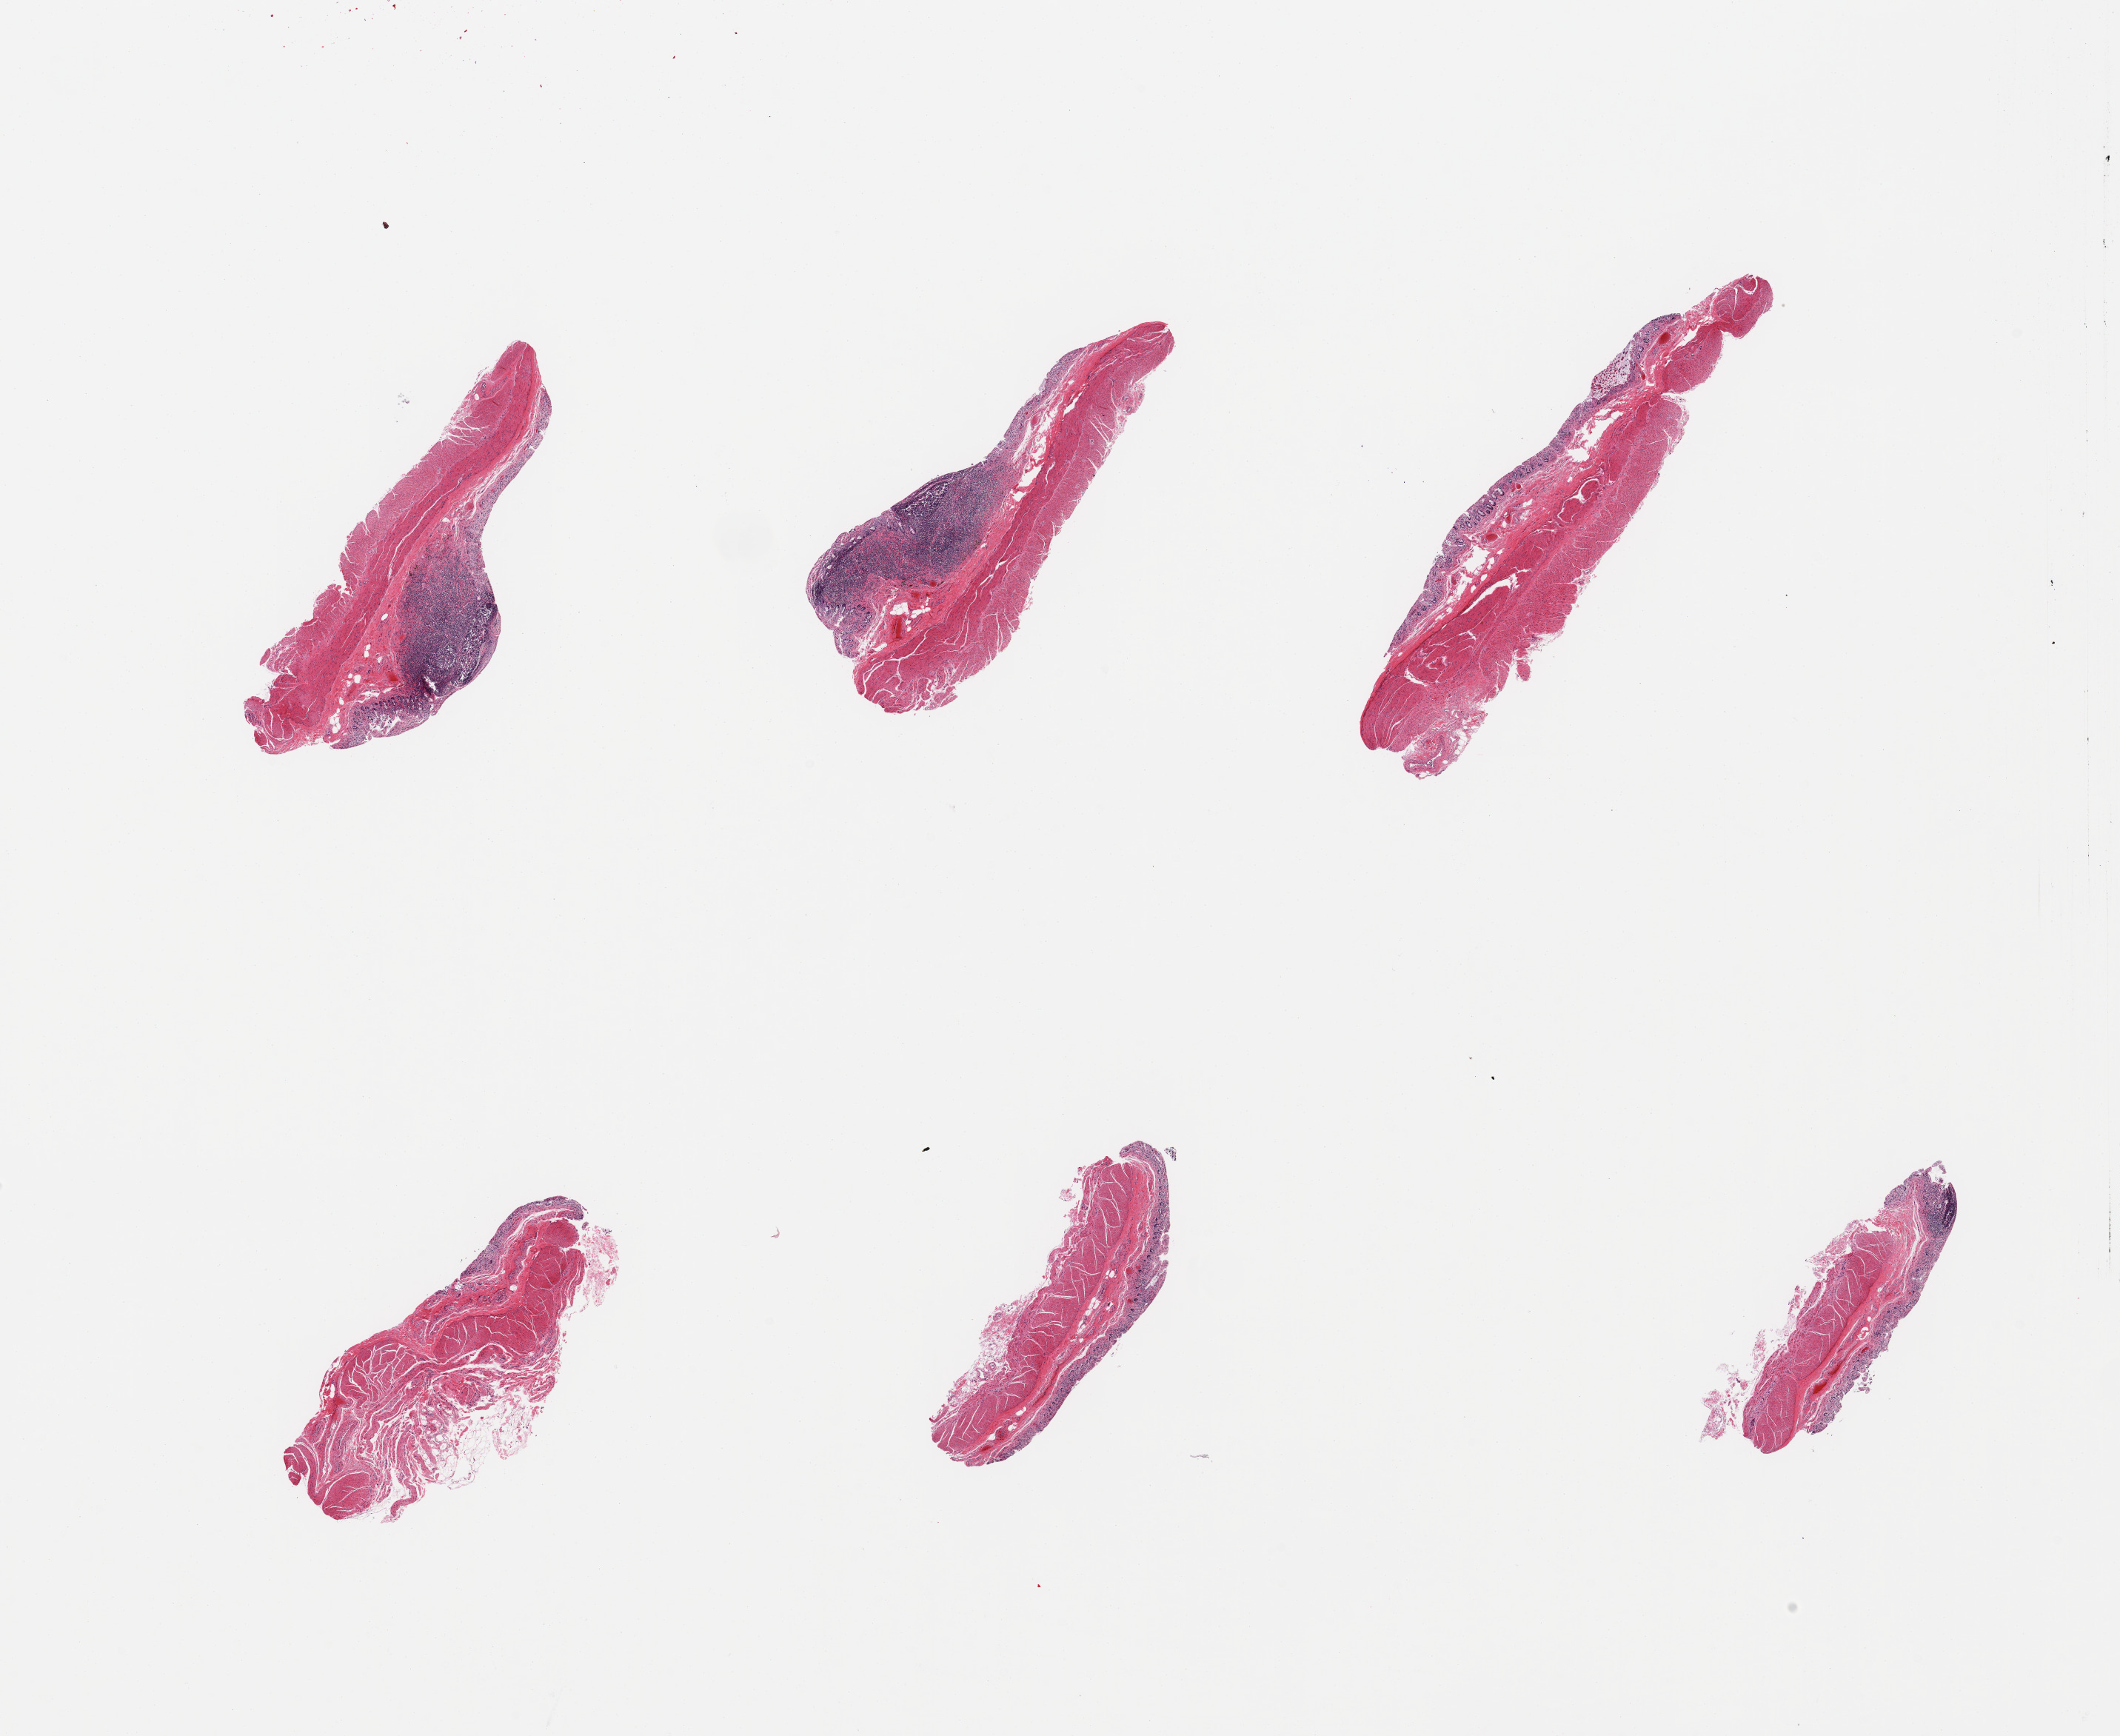
Whole-slide image, haematoxylin and eosin stain, brightfield, a low-resolution overview of the entire scanned area, about 22.6 x 18.5 mm (acquisition: 20x scan), PAXgene-fixed, paraffin-embedded tissue, target tissue: ileum, tissue donor sample. Donor: female.
Review note (as recorded): 6 pieces; full thickness (muscularis not target), mucosa partially autolyzed, only 2 pieces include good lymphoid component (insufficient).